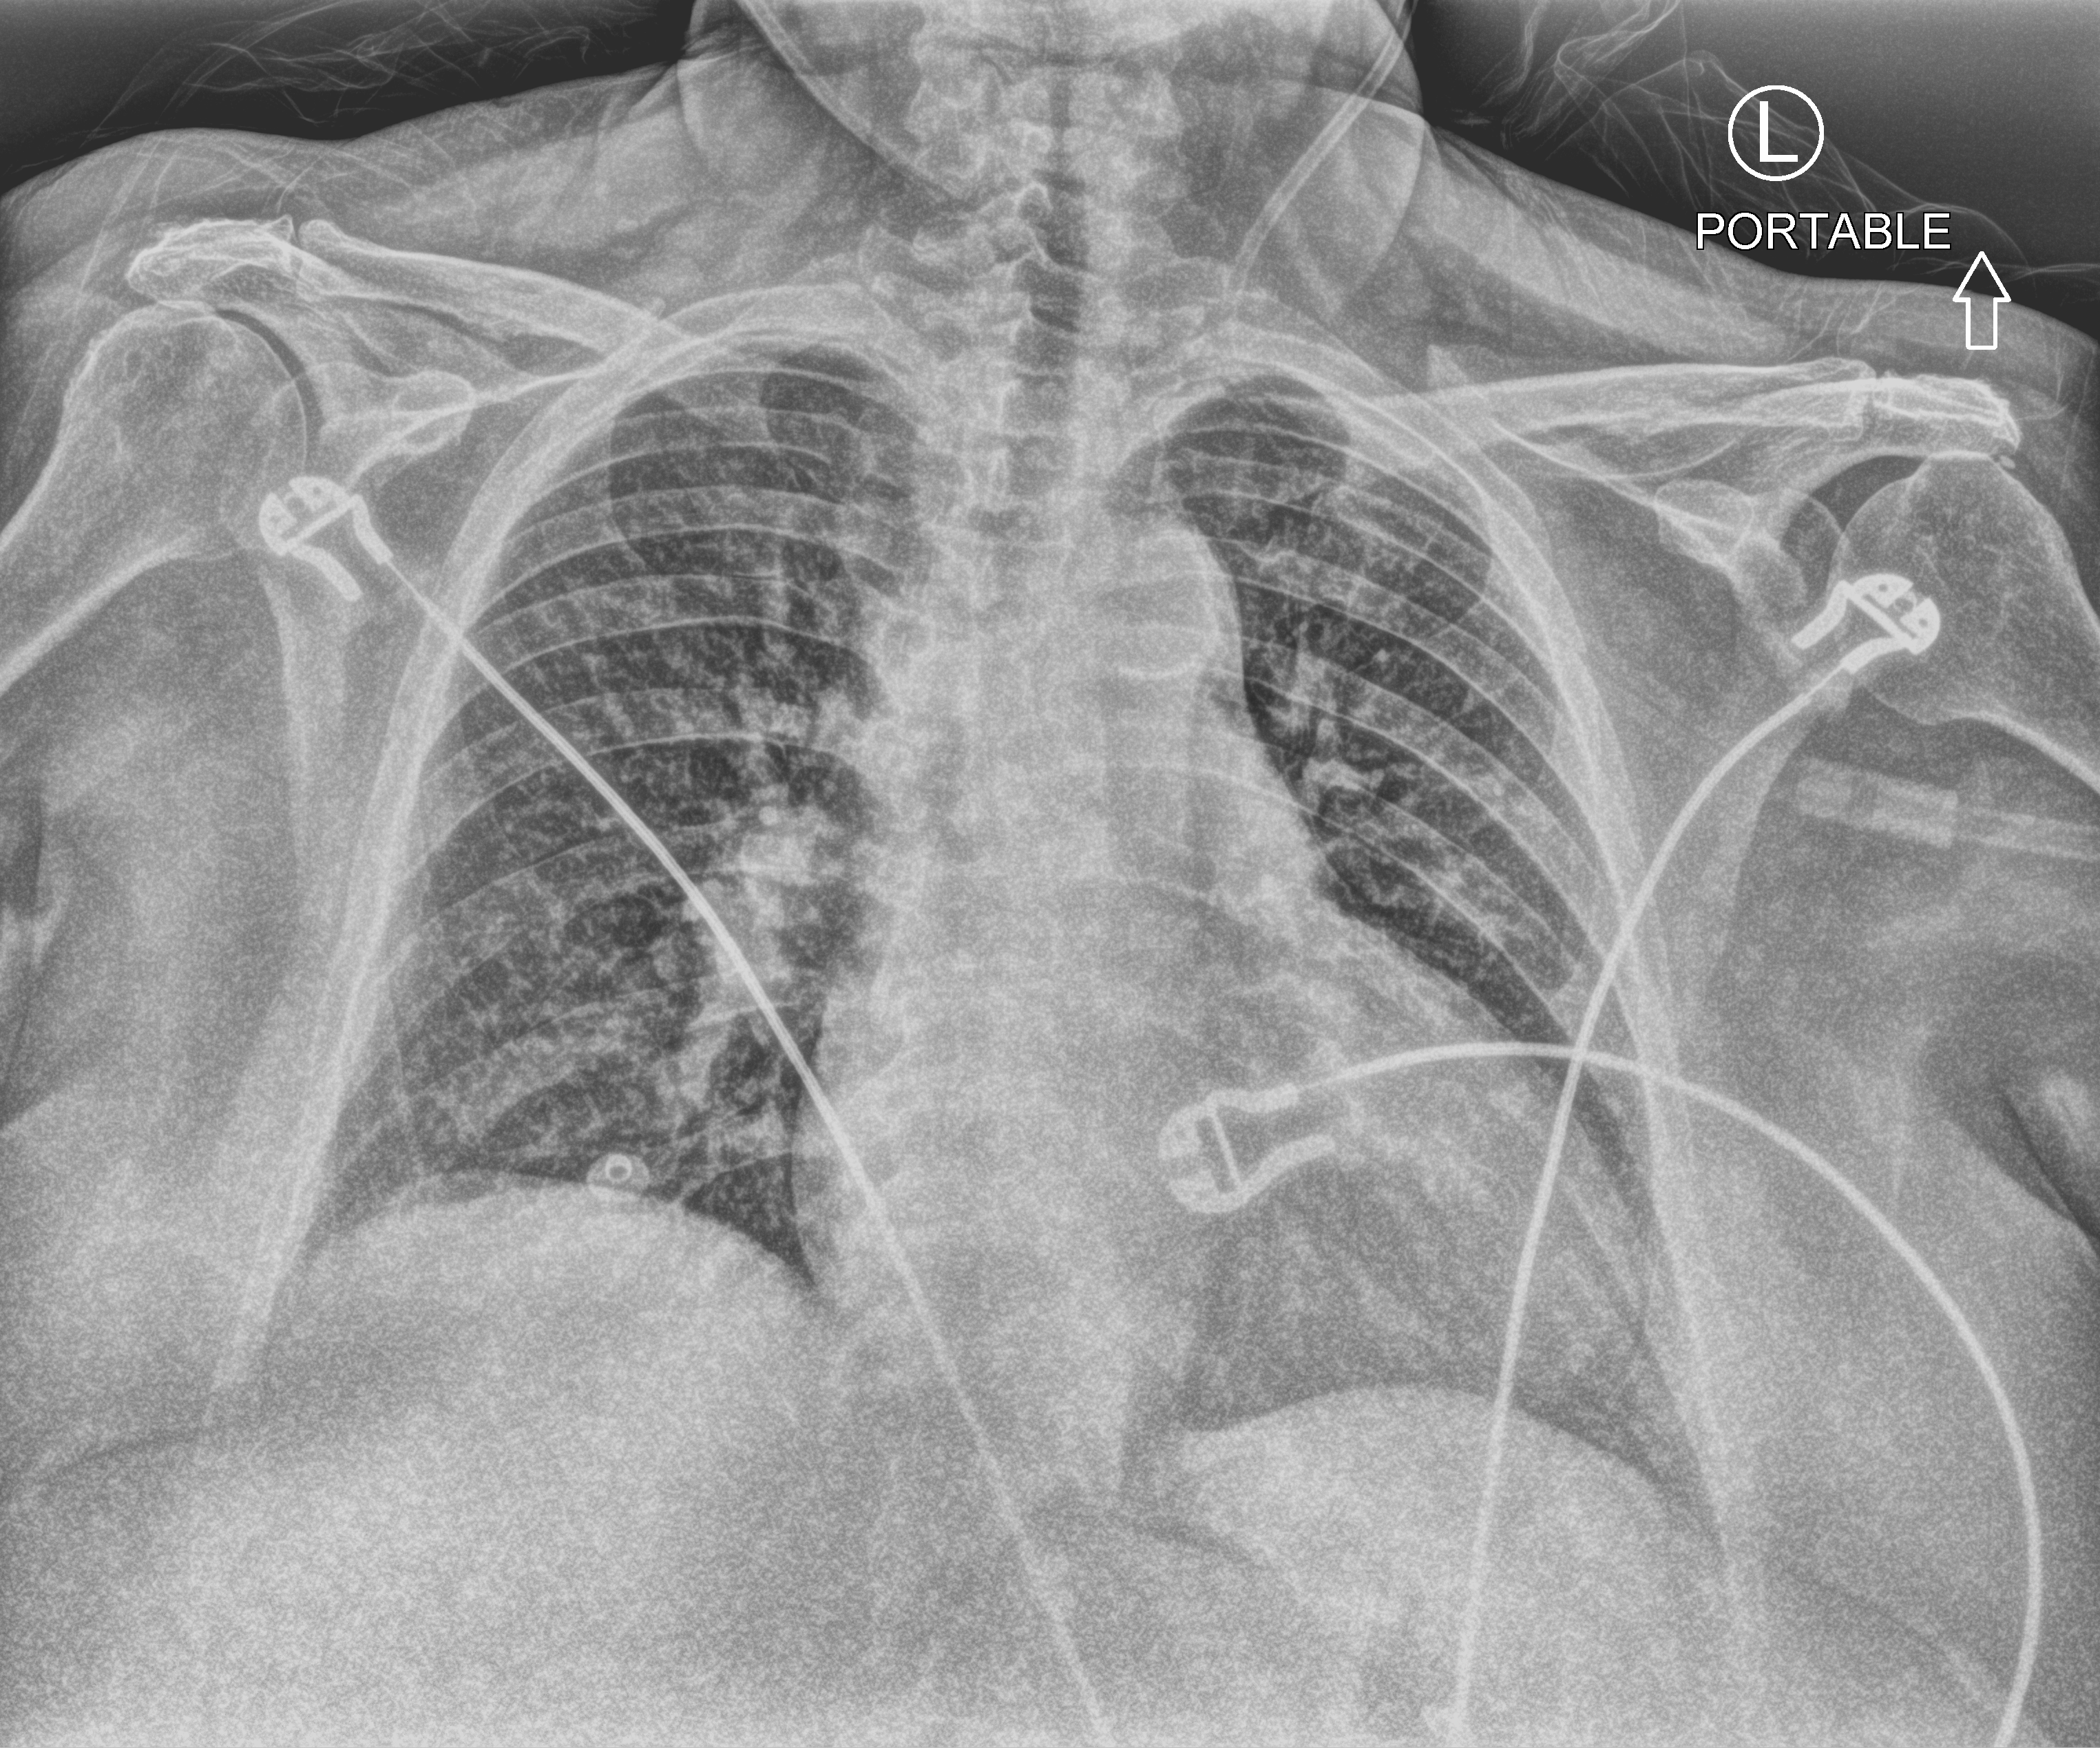
Chest X-ray (portable), anteroposterior (AP) projection. Patient hospitalised with COVID-19; female, aged 75–90 years.
From the hospital-stay record, not from the radiograph (when in the stay this image was taken is not recorded): chronic kidney disease (admission record): no.